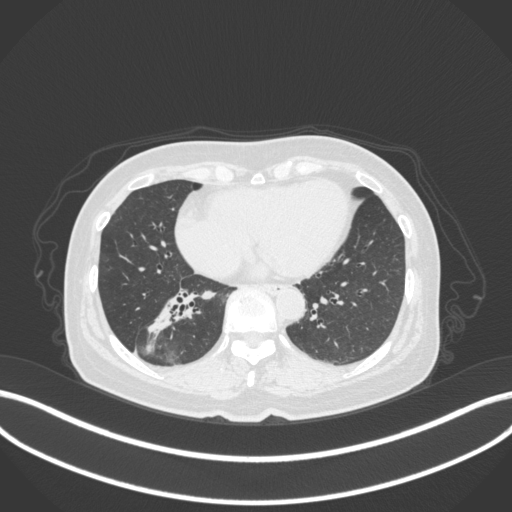
Chest CT, one axial slice; position 145 of 429 along the scan axis; reconstruction kernel B31f; 120 kVp; lung window (W 1500 / L -600 HU); 1 mm slice thickness; 512 × 512 image matrix. Patient: female, 67 years. From the clinical record (not read from this slice): clinical TNM (as recorded): T1c N1 M0; histopathological grade: G2-3.
Annotated regions visible in this slice (rectangle marked by the reading radiologist):
- lung tumour (recorded histology: adenocarcinoma): bounding box (x1, y1, x2, y2) in pixels: (135, 278, 205, 342)